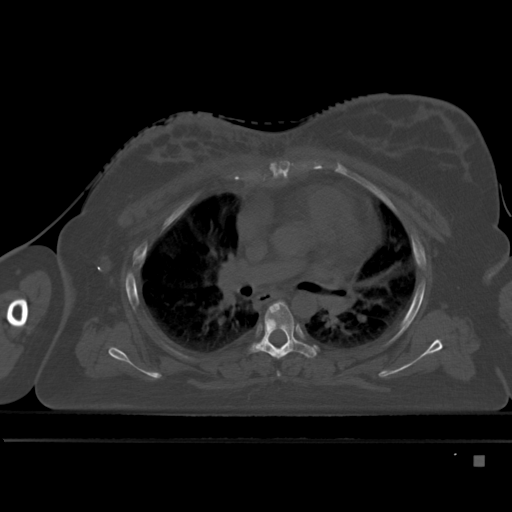
CT including the spine, one axial slice; slice 321 of 495 in the series (ordered by position); bone window (W 1800 / L 400 HU); 1.5 mm slice thickness; 512 × 512 image matrix, field of view 404 × 404 mm. Patient: female, 33 years. From the clinical record (not read from this slice): primary cancer: breast; vertebrae with lytic lesions (as recorded): T1.
Structures marked on this image (semi-automatically segmented with operator editing):
- T5 vertebra: bounding box <250,301,316,360> (left, top, right, bottom; pixels)